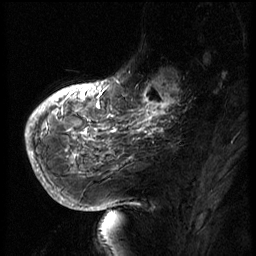
Breast MRI (dynamic contrast-enhanced), one sagittal slice. Position 17 of 66 along the scan axis. 3 images stored at this slice position (order not interpretable as contrast timing). 1.5 T. TE 4.2 ms, TR 8.9 ms. 2.5 mm slice thickness. 256 × 256 image matrix. Female patient, age 56 years. From the clinical record (not read from this slice): setting: breast cancer imaged before/during neoadjuvant chemotherapy.
Outlined on this slice (semi-automatically segmented with operator editing):
- analysis volume of interest (the breast-tissue region the enhancement analysis was run in; not a lesion): bounding box <129,62,194,127> (left, top, right, bottom; pixels)
- tumour enhancement mask (voxels above the 140 % enhancement threshold inside the analysis volume of interest): <130,73,182,127>